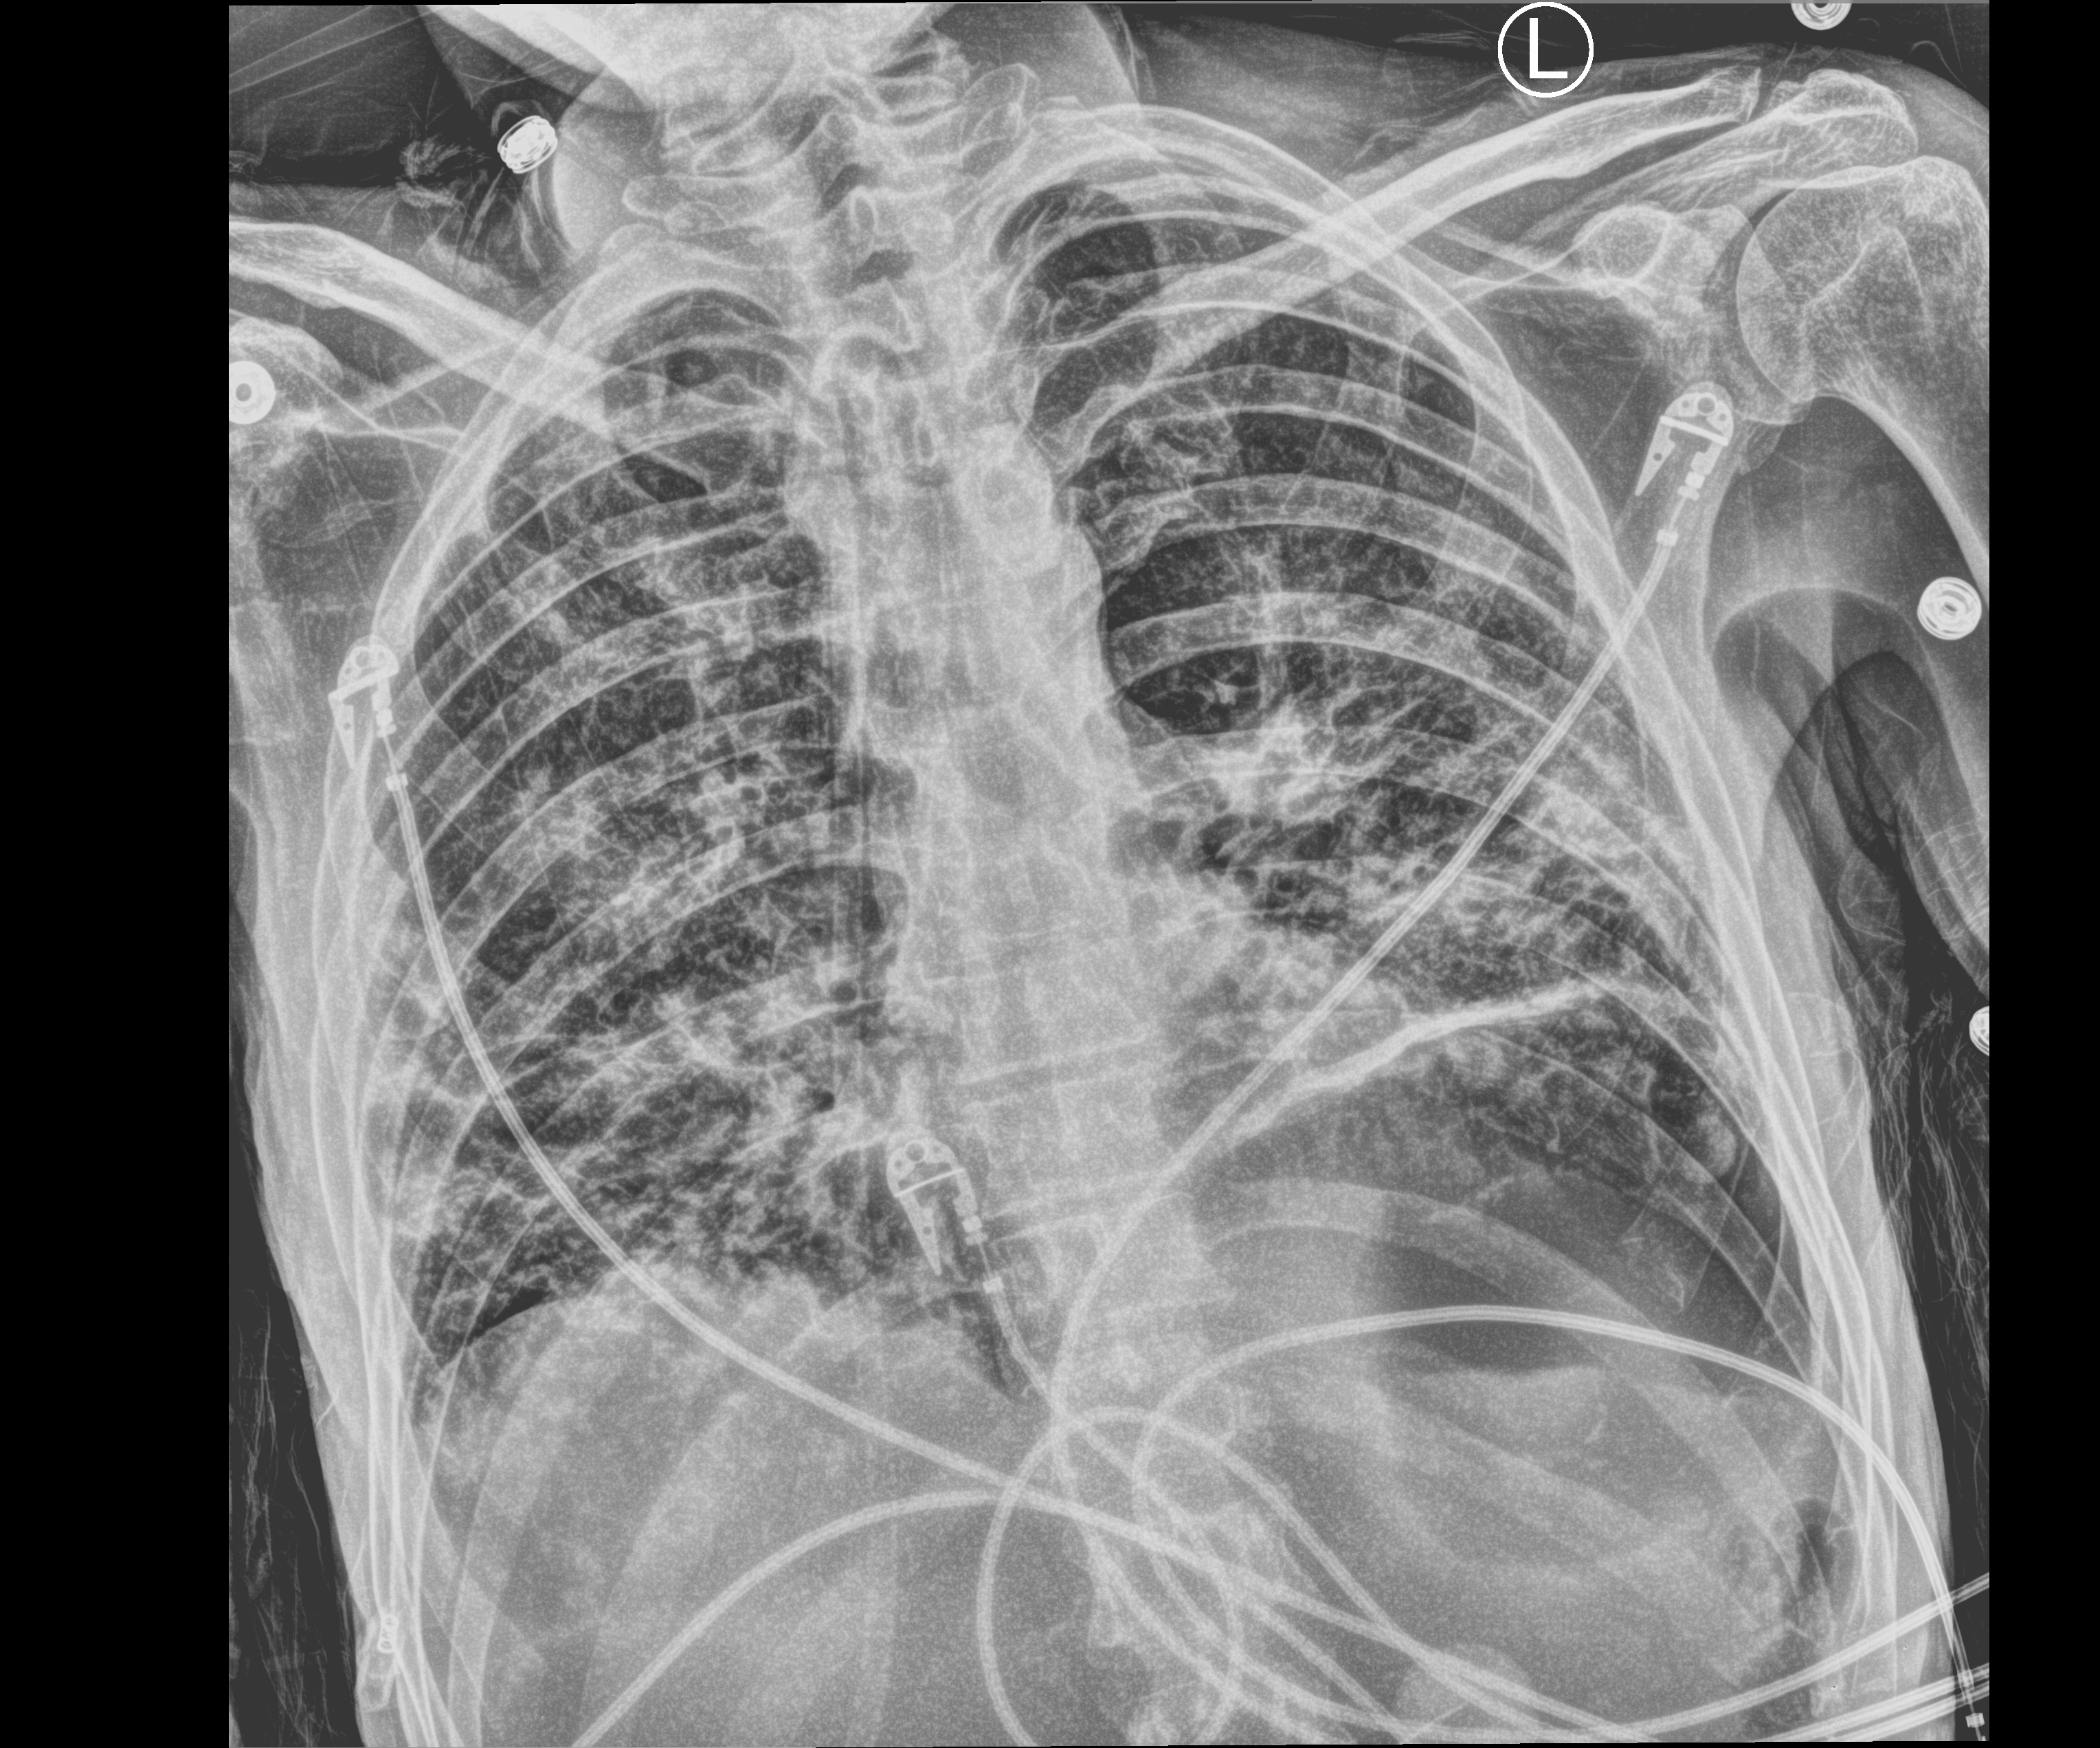
Chest X-ray (portable). Male patient hospitalised with COVID-19, age 18–59 years.
Admission-level facts for this patient (not findings on this image; timing relative to this image not recorded):
- diabetes (admission record): yes